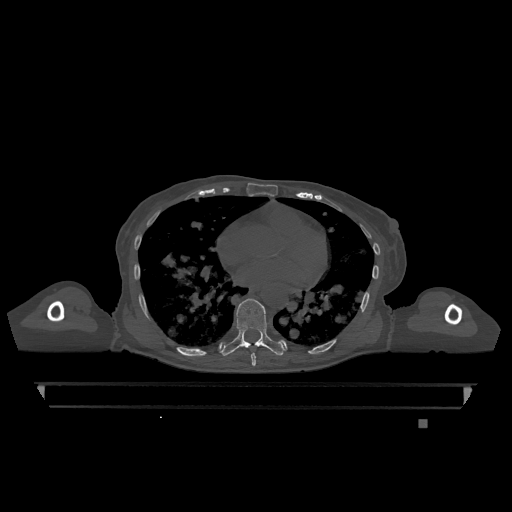
CT including the spine, one axial slice. Slice 700 of 1317 in the series (ordered by position). Bone window (W 1800 / L 400 HU). 512 × 512 image matrix, field of view 500 × 500 mm. Female patient, age 74 years. Case-level facts recorded for this patient, not image findings: primary cancer: lung; vertebrae with lytic lesions (as recorded): T1, T4, T5, T6, L4, L5.
Structures marked on this image (semi-automatic segmentation, software-assisted and operator-edited):
- T7 vertebra: bounding box (x1, y1, x2, y2) in pixels: (251, 353, 256, 366)
- T9 vertebra: (221, 298, 284, 356)